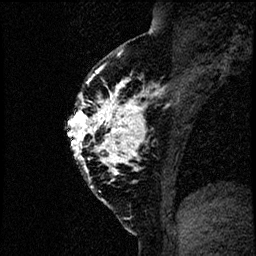
Breast MRI (dynamic contrast-enhanced), one sagittal slice; position 40 of 60 along the scan axis; dynamic contrast-enhanced study with each time point stored as its own series, time point 2 of 4 at this slice position (early post-contrast, ordered by acquisition time); 1.5 T; TE 4.2 ms, TR 17.6 ms; 2 mm slice thickness; 256 × 256 image matrix, field of view 200 × 200 mm. Patient: female, 40 years. From the clinical record (not read from this slice): setting: breast cancer imaged before/during neoadjuvant chemotherapy; receptor status: HER2-positive.
Outlined on this slice (semi-automatic segmentation, software-assisted and operator-edited):
- analysis volume of interest (the breast-tissue region the enhancement analysis was run in; not a lesion): bounding box [x1, y1, x2, y2] px = [66, 55, 185, 206]
- tumour enhancement mask (voxels above the 100 % enhancement threshold inside the analysis volume of interest): [67, 81, 141, 168]